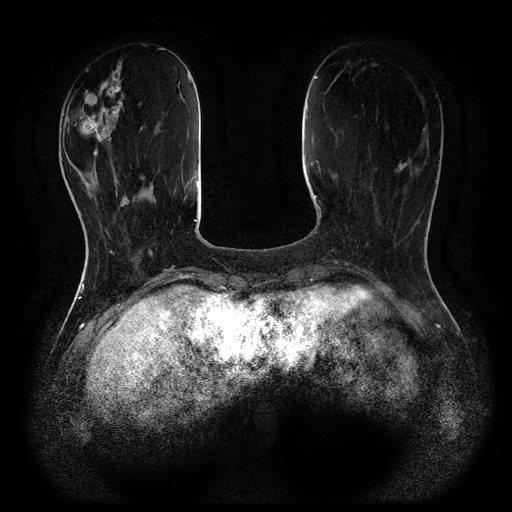
Breast MRI (dynamic contrast-enhanced, multi-phase), one axial slice; dynamic contrast-enhanced series, time point 2 of 5 at this slice position (early post-contrast); 1.5 T; TE 2.6 ms, TR 5.4 ms; 2 mm slice thickness; 512 × 512 image matrix. Patient: female, 48 years.
Annotated regions visible in this slice (semi-automatic segmentation, software-assisted and operator-edited):
- breast lesion (labelled benign in the annotation): bounding box <67,59,125,149> (left, top, right, bottom; pixels)